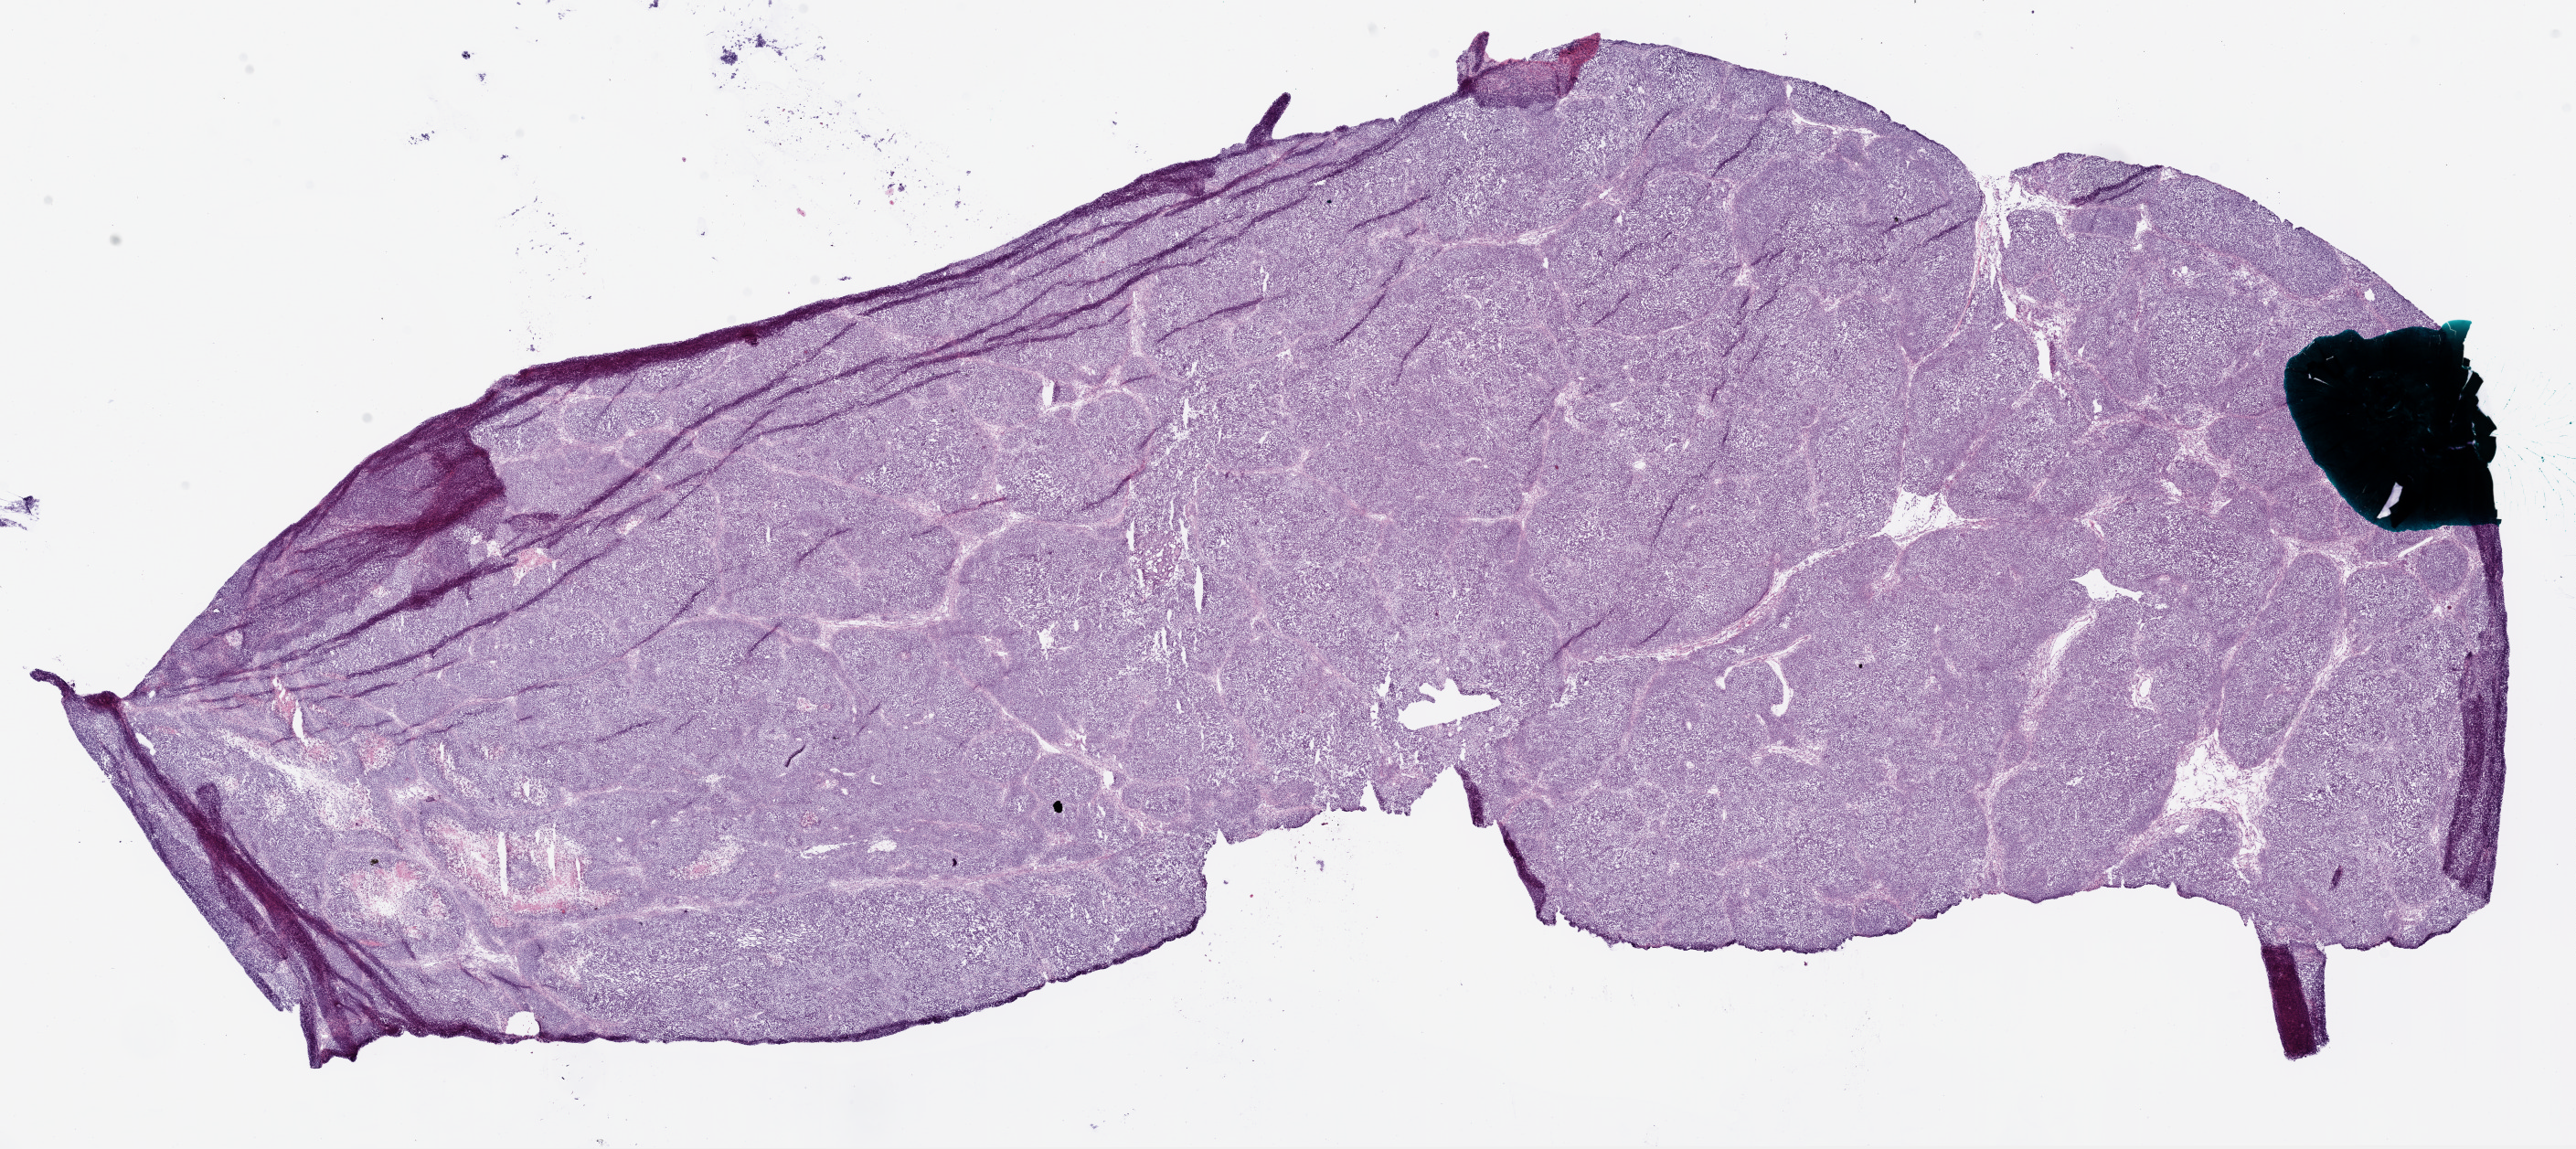
Digitized H&E tissue section (whole slide) — low-resolution overview of the scanned area, about 22.7 x 10.1 mm (slide scanned at 20x). Frozen section. Primary tumour sample from the ovary. Female patient; age at initial diagnosis 55 years. Histologic grade: G3 (poorly differentiated). Composition of this section per pathologist review: tumour cells 95%, tumour nuclei 98%, normal cells 0%, stromal cells 5%, necrosis 0%.
Laterality: right. Histologic diagnosis: Serous cystadenocarcinoma, NOS. FIGO stage: IIIC.